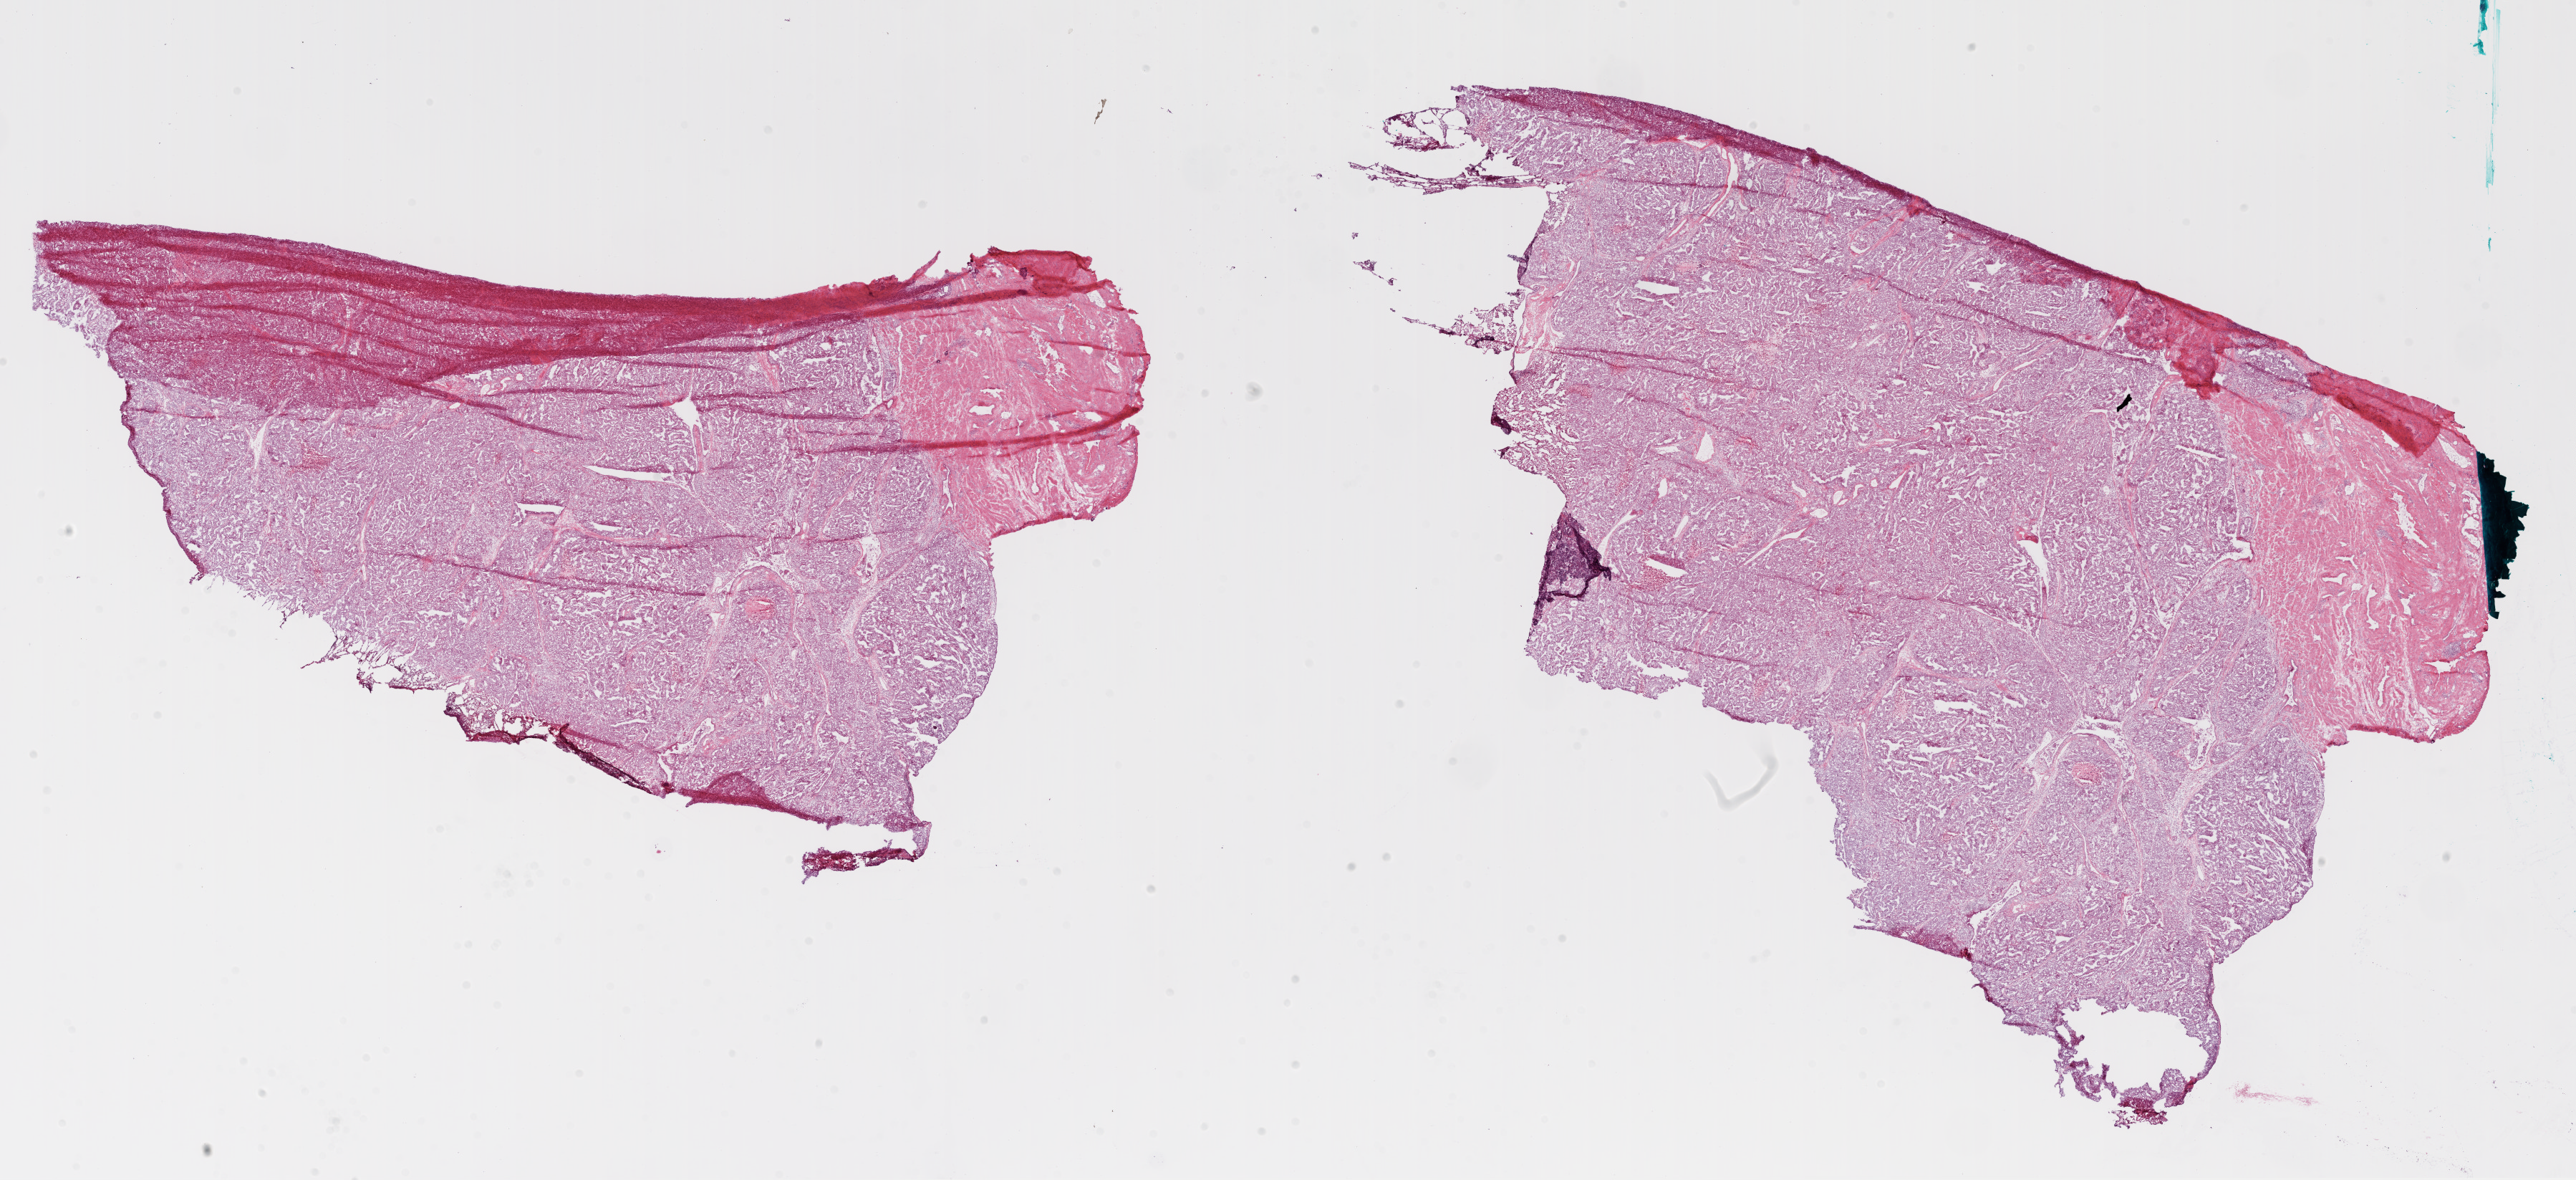
H&E whole-slide image — low-resolution overview of the scanned area, about 29.0 x 13.3 mm (from a 20x scan), frozen section from the bottom of the tissue portion, sample: primary tumour, ovary. Female, age 74 years at initial diagnosis. Histologic grade: G3 (poorly differentiated). Pathologist review of this section (percent, as recorded): tumour cells 90%, tumour nuclei 95%, normal cells 0%, stromal cells 10%, necrosis 0%. Infiltration values recorded for this section: lymphocyte infiltration 20%.
Pathologic diagnosis: Serous cystadenocarcinoma, NOS. FIGO stage: IIIC.